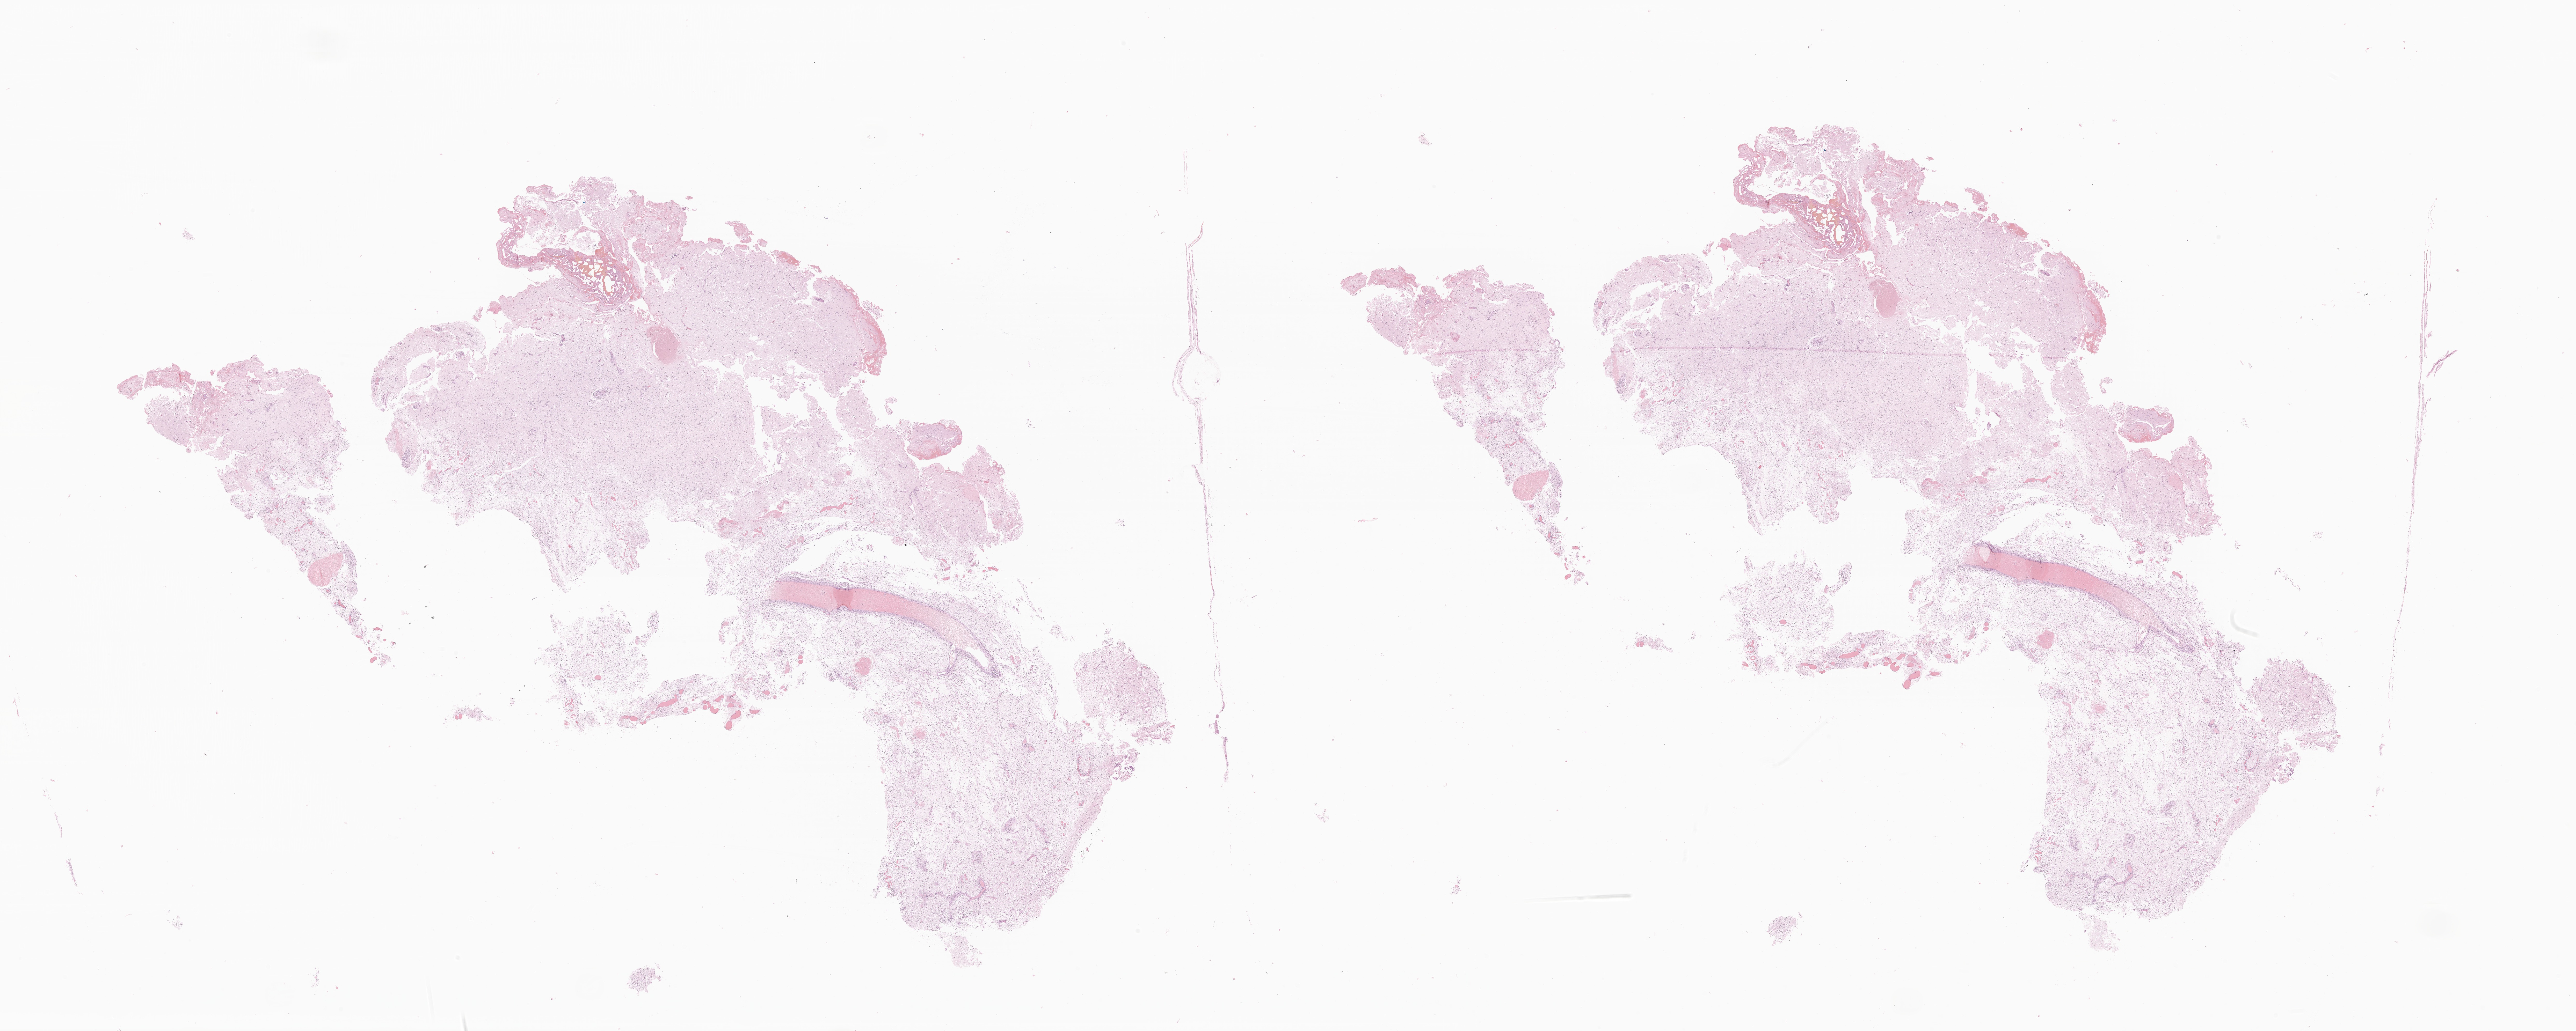
Whole-slide image, H&E stain of tumor tissue from the brain, a low-resolution overview of the entire scanned area, about 41.9 x 16.8 mm; formalin-fixed, paraffin-embedded (FFPE) tissue. Patient: female, age 147 months (12 years 3 months).
Diagnosis (ICD-O-3 morphology term): Ganglioglioma, NOS.